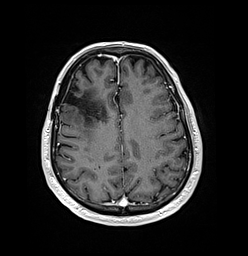
Brain MRI from a brain-tumour surgery series, one axial slice; slice 55 of 176 in the series (ordered by position); T1-weighted post-contrast; 248 × 256 image matrix, field of view 242 × 250 mm. From the clinical record (not read from this slice): histopathology: Oligodendroglioma; WHO grade: 3; IDH mutation: yes; tumour location: Right Frontal.
Structures marked on this image (expert manual segmentation):
- previous resection cavity: box from (x=64, y=91) to (x=81, y=107) px